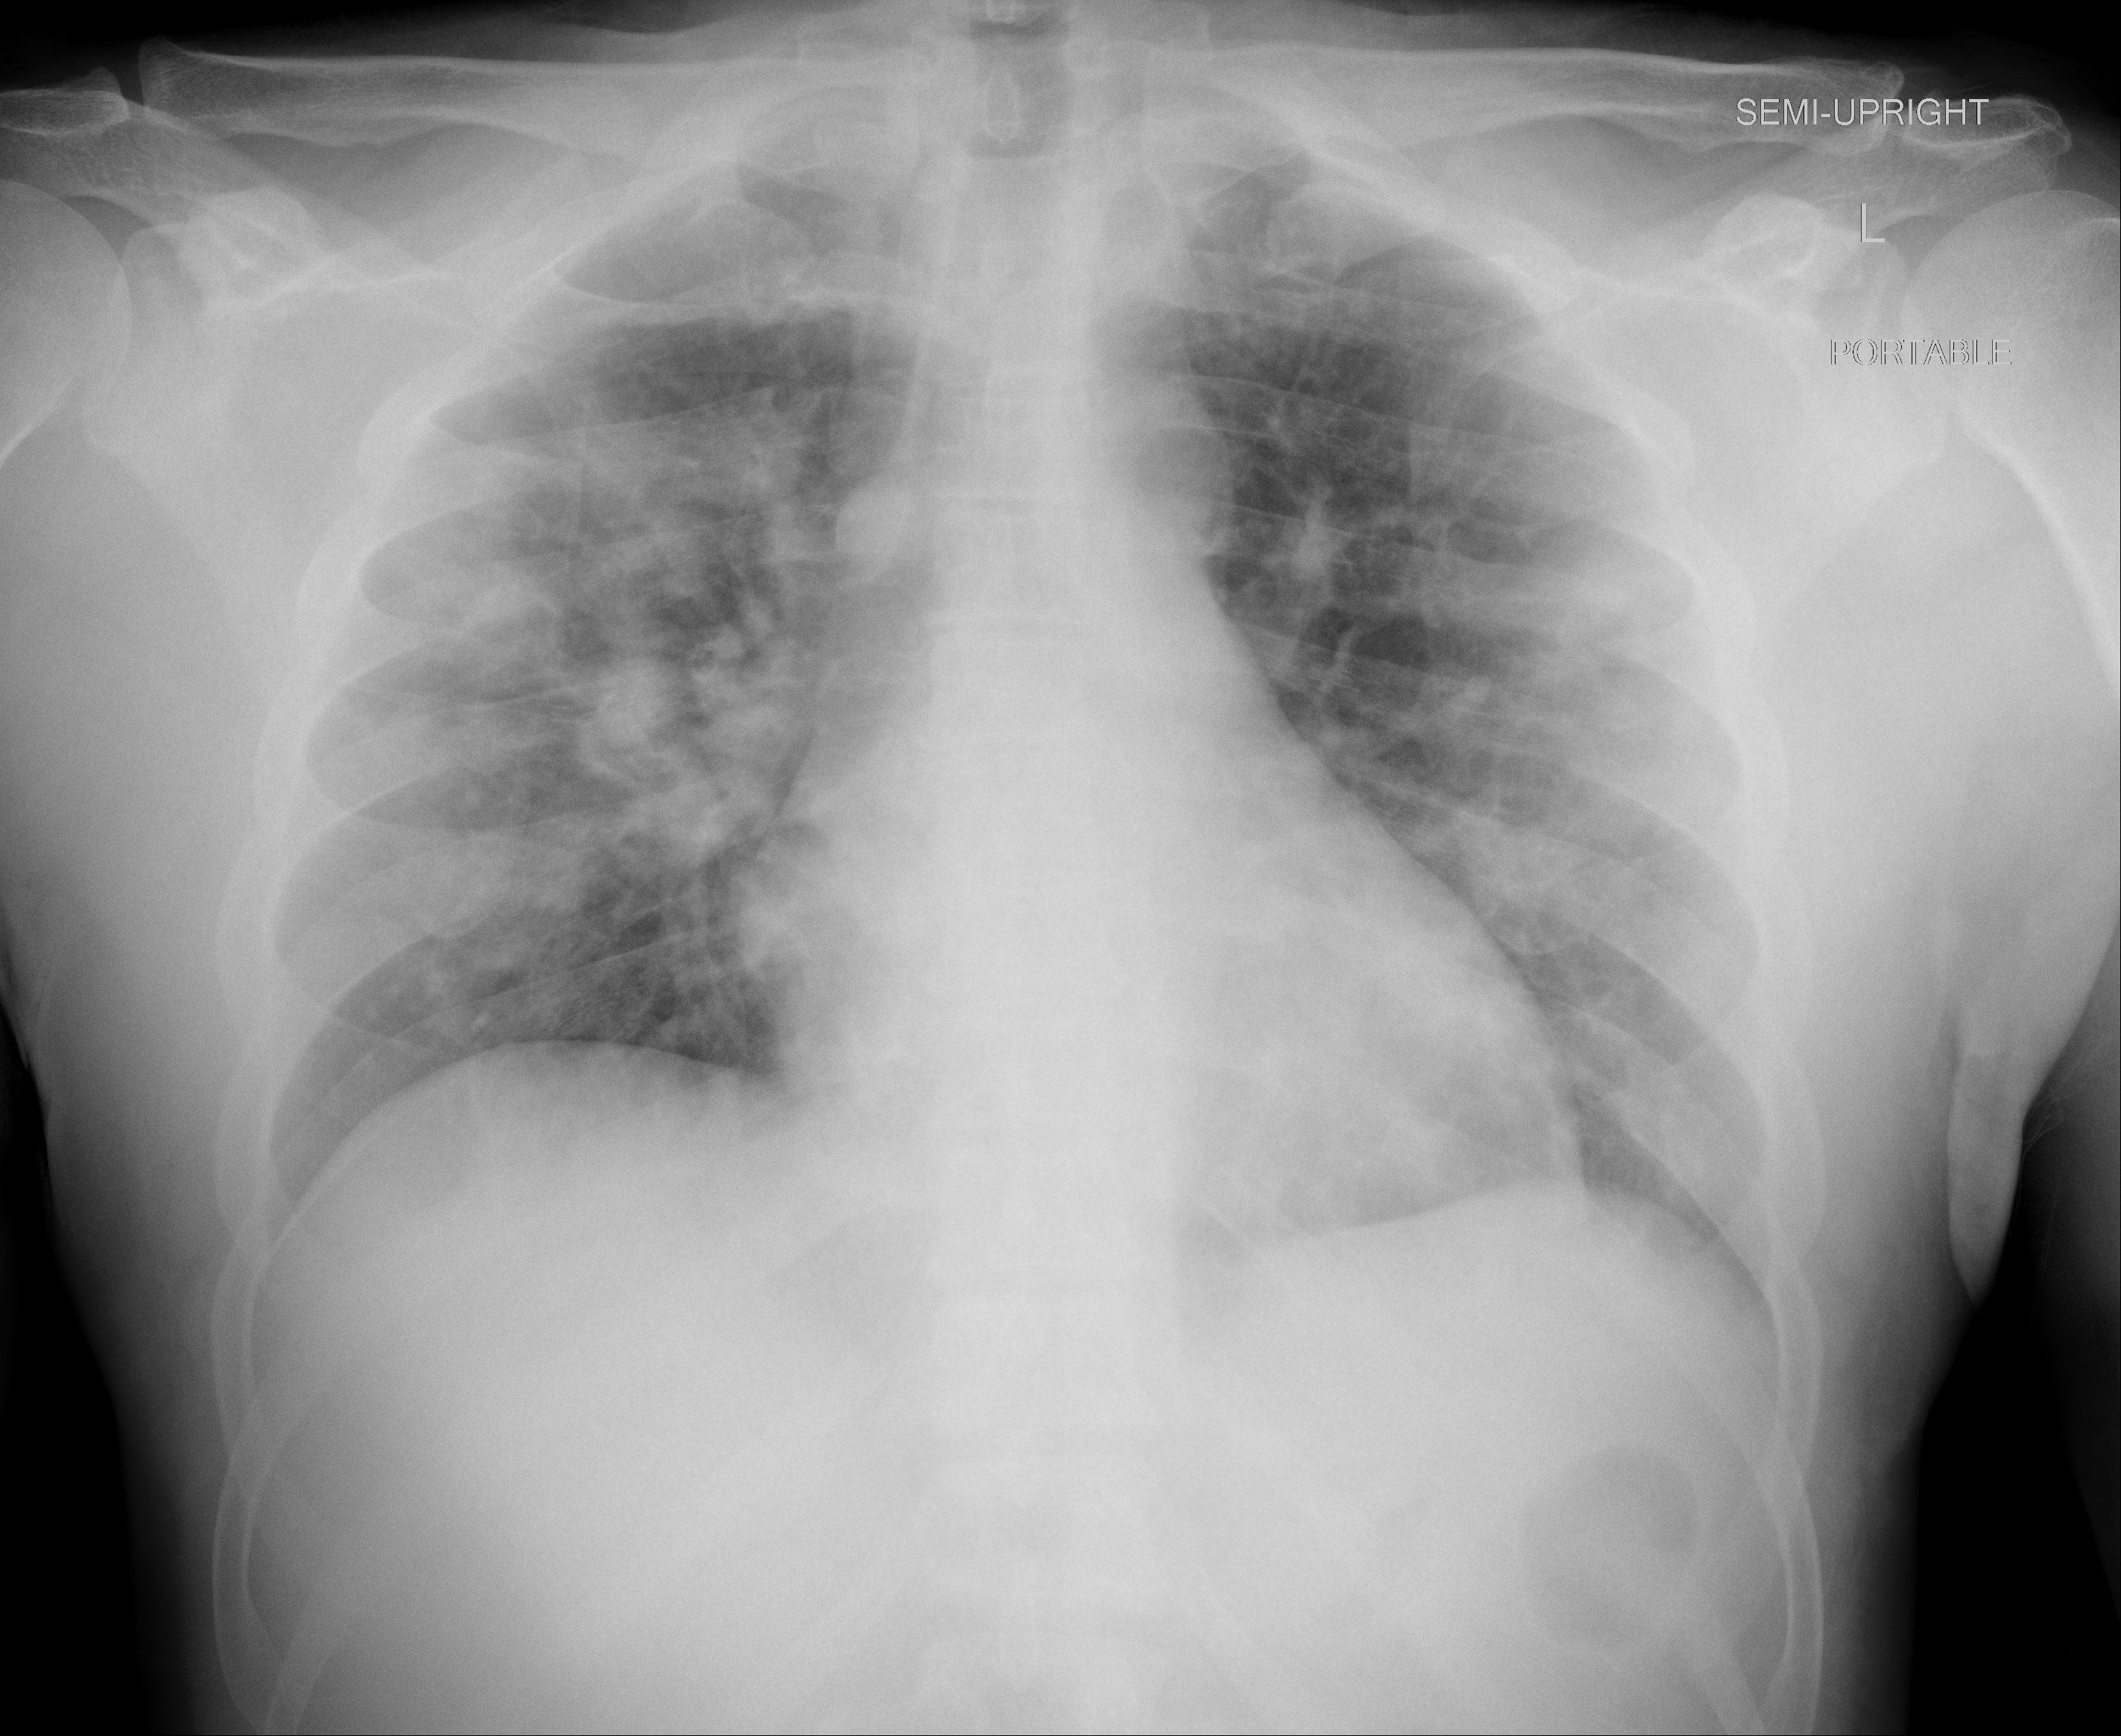
Chest radiograph, AP projection. Male patient, age 48 years; imaged 4 days after the COVID-19 diagnosis.
Radiologist key findings (as recorded): Essentially stable bilateral patchy ground-glass and consolidative opacities throughout both lungs.